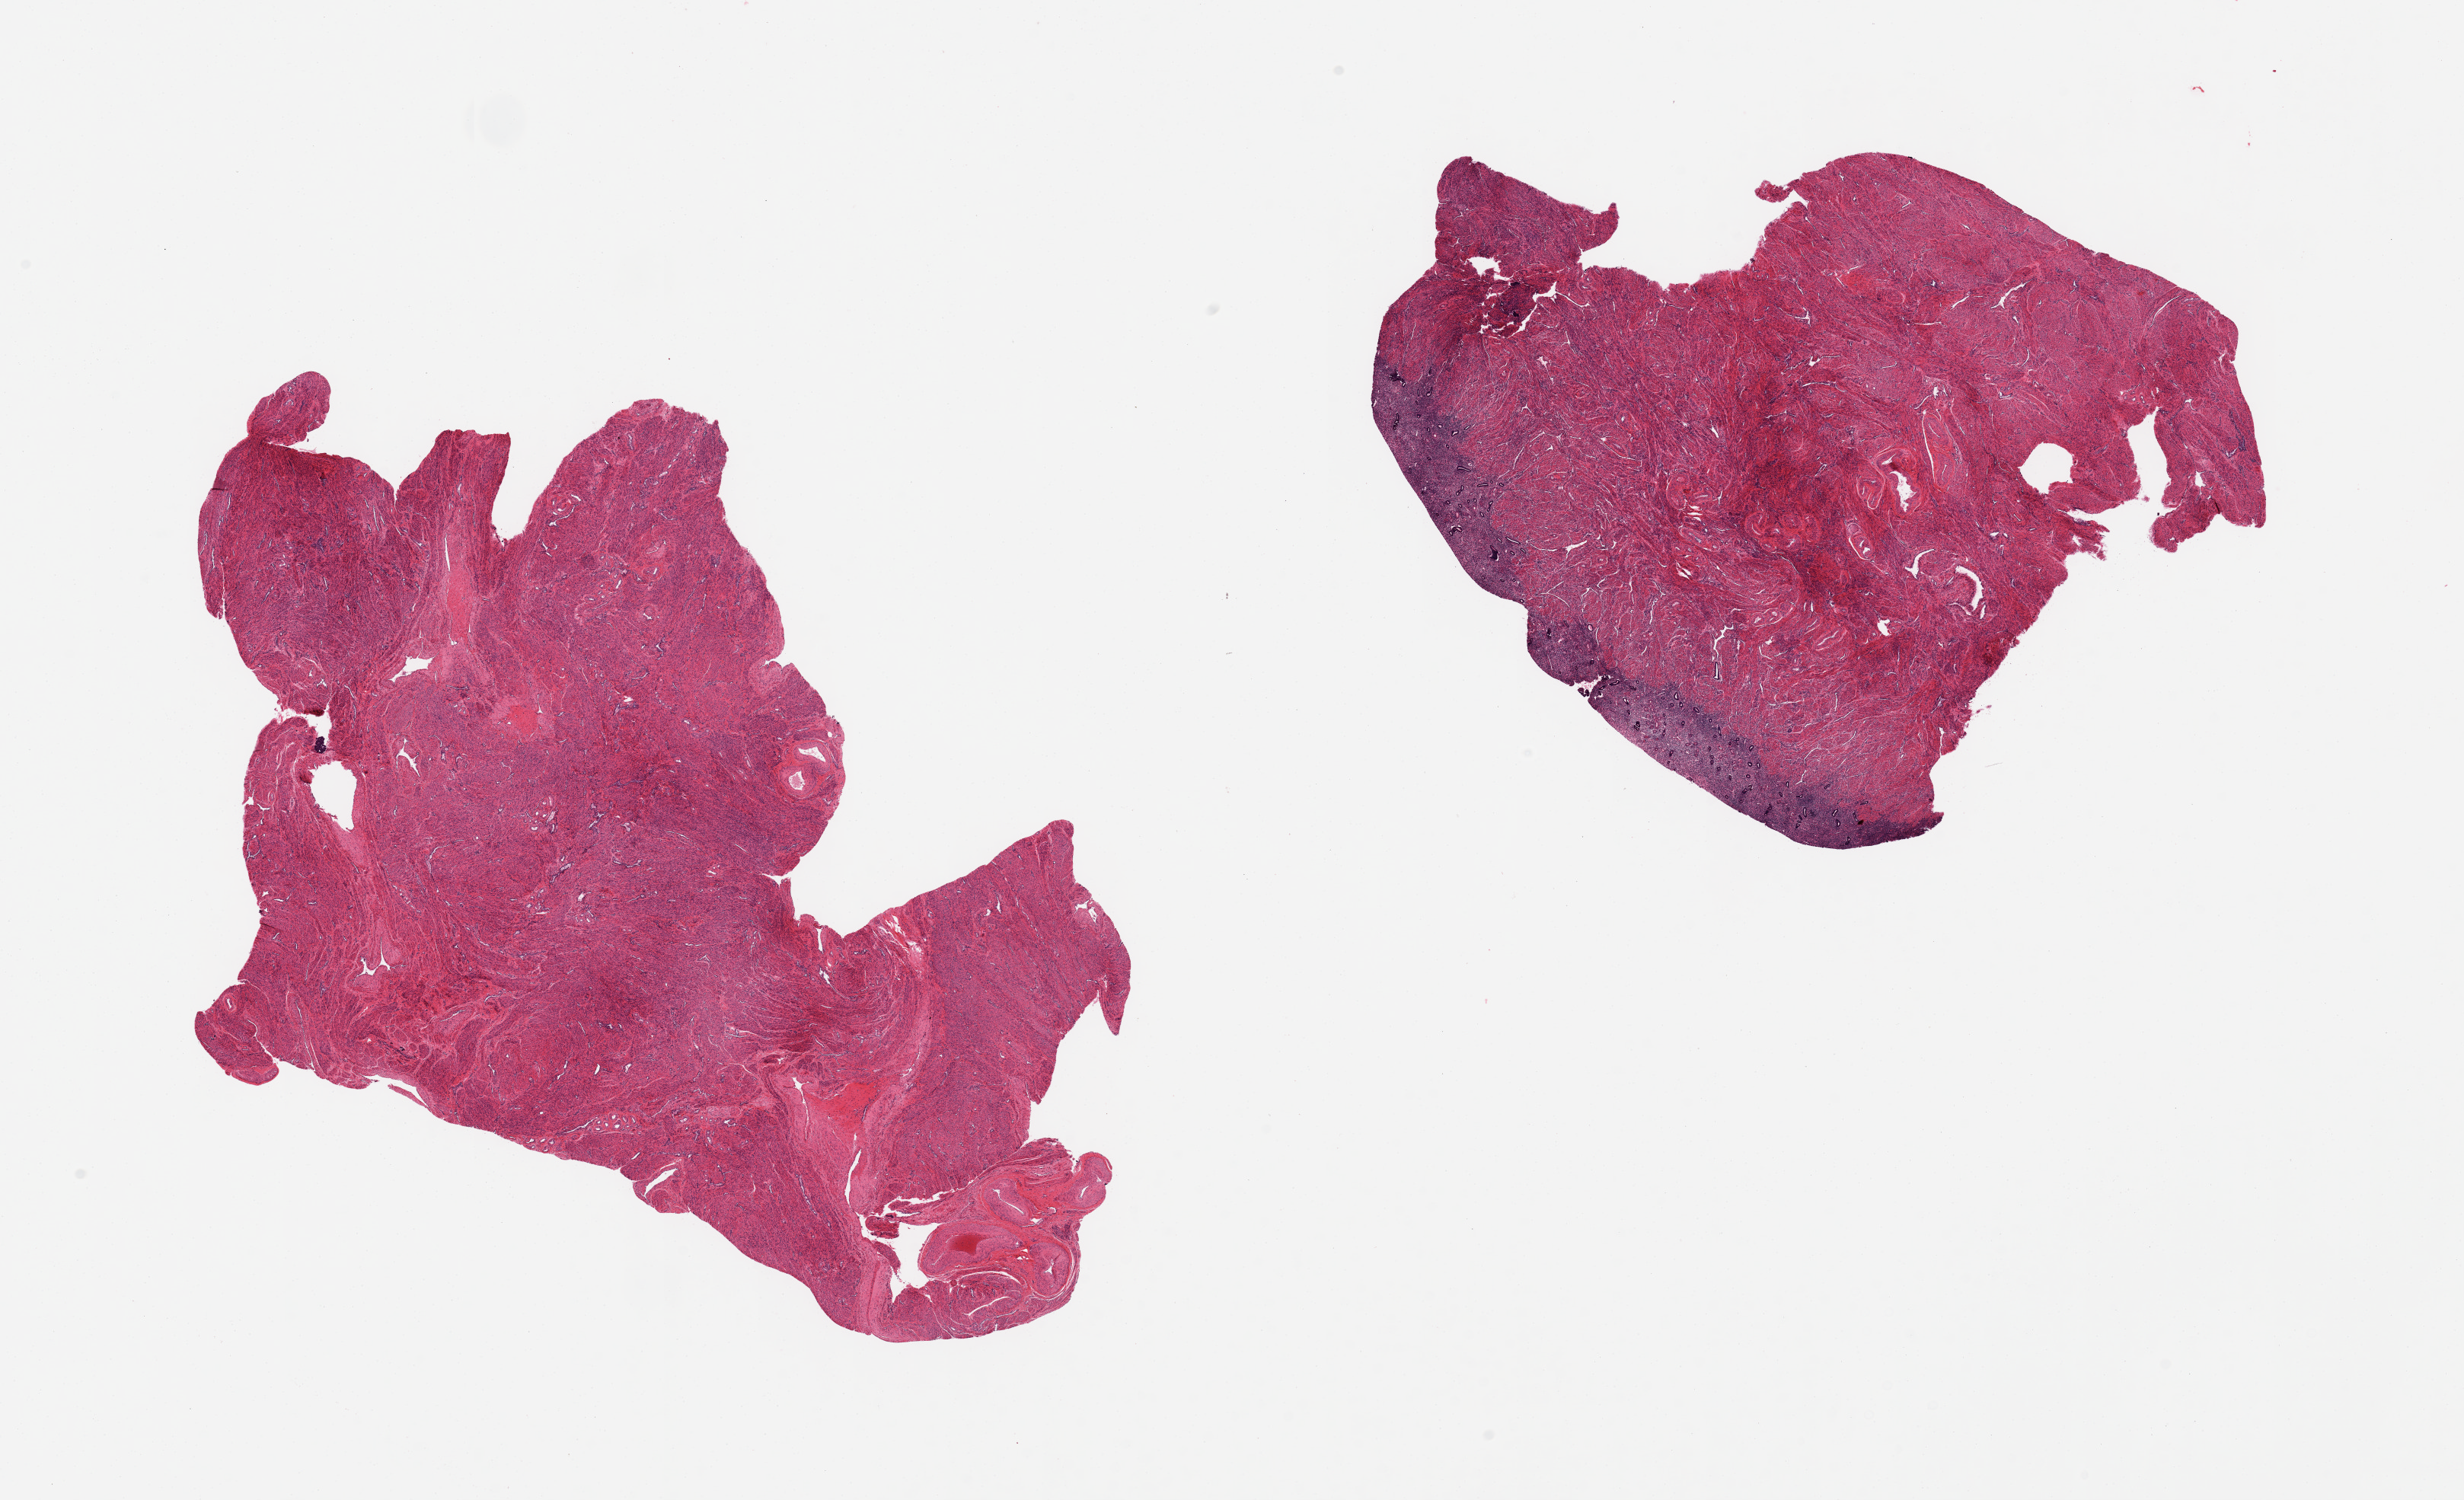
Whole-slide image, hematoxylin and eosin (H&E) stain — low-resolution overview of the scanned area, about 25.6 x 15.6 mm (slide scanned at 20x); PAXgene-fixed, paraffin-embedded tissue; target tissue: uterus; tissue donor sample. Donor: female.
• review note (as recorded): 2 pieces; 0.8mm thin inactive endometrium on 1 piece; only myometrium visualized on other